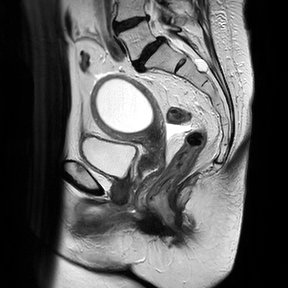
Pelvic MRI for cervical cancer, one sagittal slice; T2-weighted; 1.5 T; TE 100 ms, TR 4816.3 ms; 288 × 288 image matrix. Female patient, age 74 years.
Annotated regions visible in this slice (expert manual segmentation):
- uterus and cervix: bounding box (x1, y1, x2, y2) in pixels: (90, 74, 165, 180)